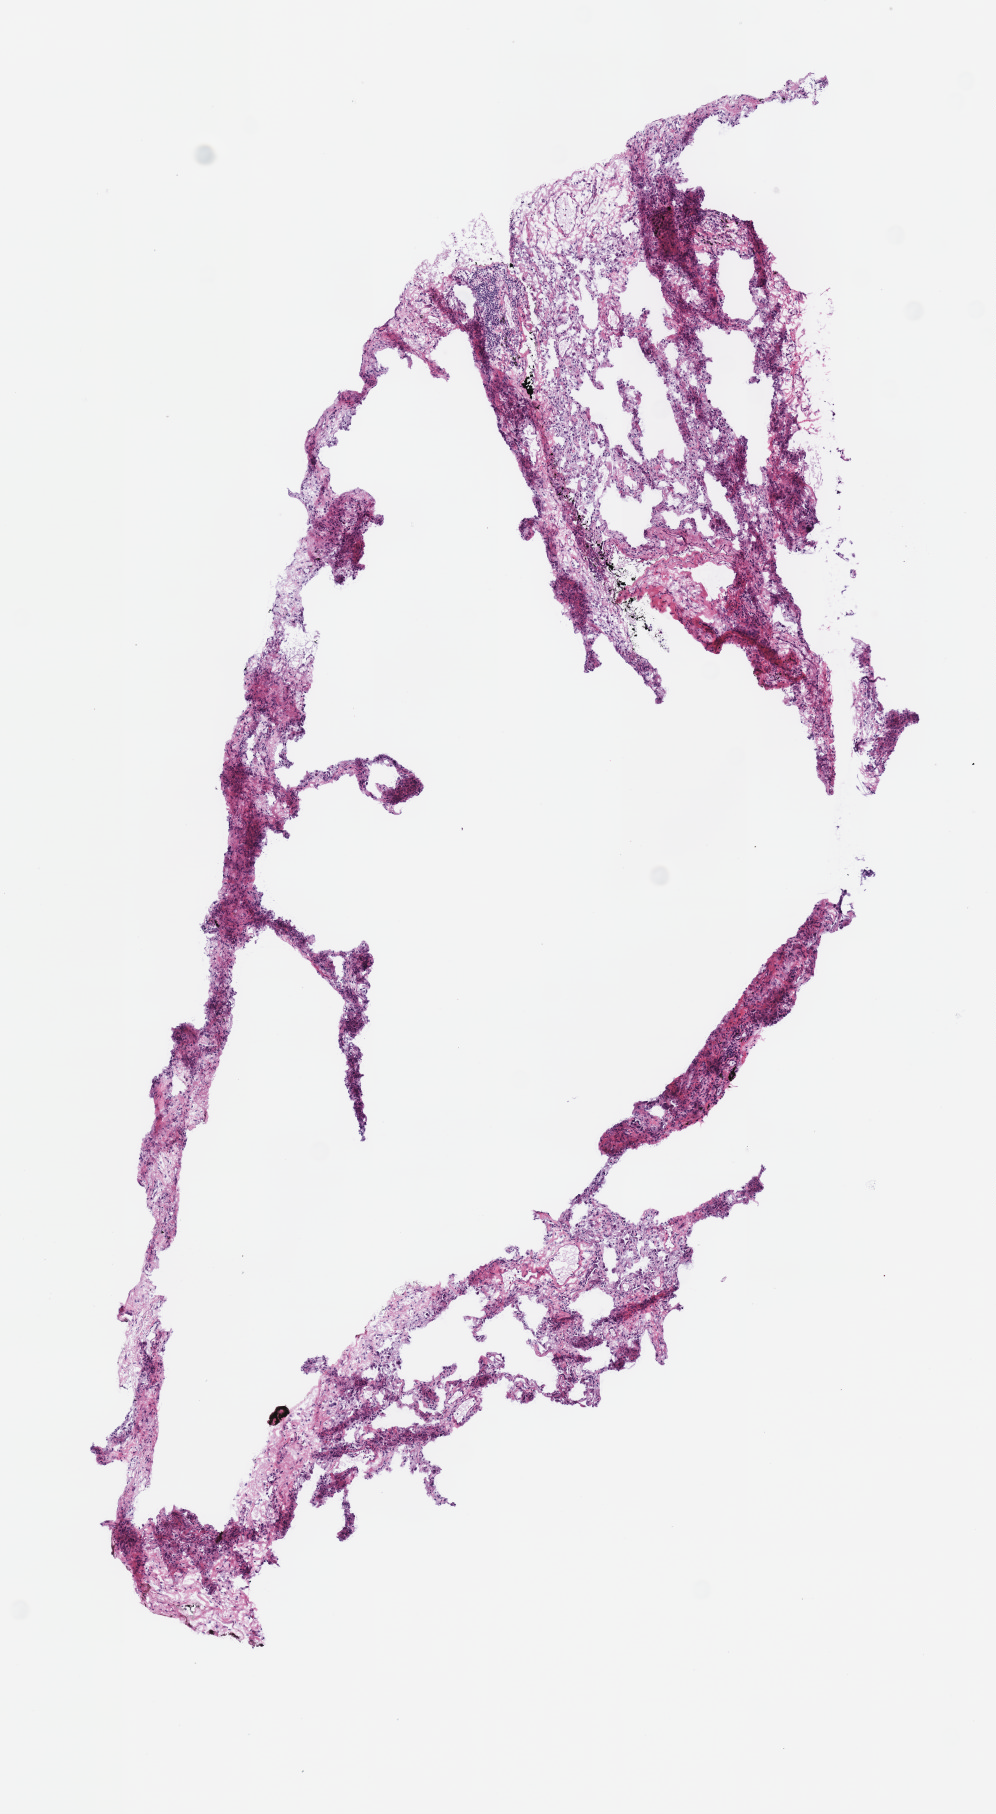
Whole-slide histology image, H&E, whole scanned area (about 3.9 x 7.1 mm, acquisition: 40x scan) shown as a low-resolution overview, frozen section from the top of the tissue portion, solid tissue normal (non-tumour tissue) sample from the lung. Female patient; age at initial diagnosis 75 years.
This section: solid tissue normal (non-tumour) sample from the same patient. Patient diagnosis: Adenocarcinoma, NOS (lower lobe, lung).